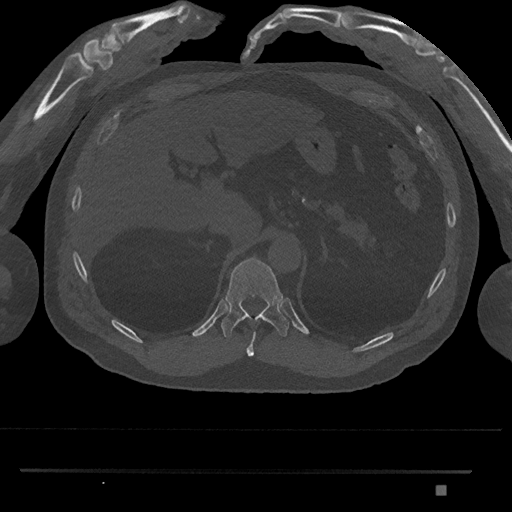
CT including the spine, one axial slice; slice 957 of 1134 in the series (ordered by position); 120 kVp; bone window (W 1800 / L 400 HU); 0.5 mm slice thickness; 512 × 512 image matrix, field of view 429 × 429 mm. Male patient, age 65 years. Case-level facts recorded for this patient, not image findings: primary cancer: prostate.
Annotated regions visible in this slice (semi-automatic segmentation, software-assisted and operator-edited):
- T10 vertebra: bounding box [x1, y1, x2, y2] px = [246, 331, 256, 357]
- T11 vertebra: [221, 257, 289, 338]